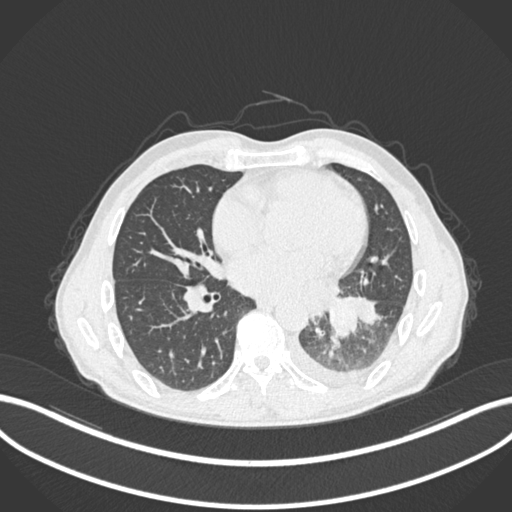
Chest CT, one axial slice. 120 kVp. Lung window (W 1500 / L -600 HU). 1 mm slice thickness. 512 × 512 image matrix, field of view 400 × 400 mm. Patient: male, 47 years. From the clinical record (not read from this slice): clinical TNM (as recorded): T3 N1 M1c; histopathological grade: G3.
Annotated regions visible in this slice (bounding box drawn by a radiologist):
- lung tumour (recorded histology: small cell carcinoma): bounding box <325,289,362,338> (left, top, right, bottom; pixels)